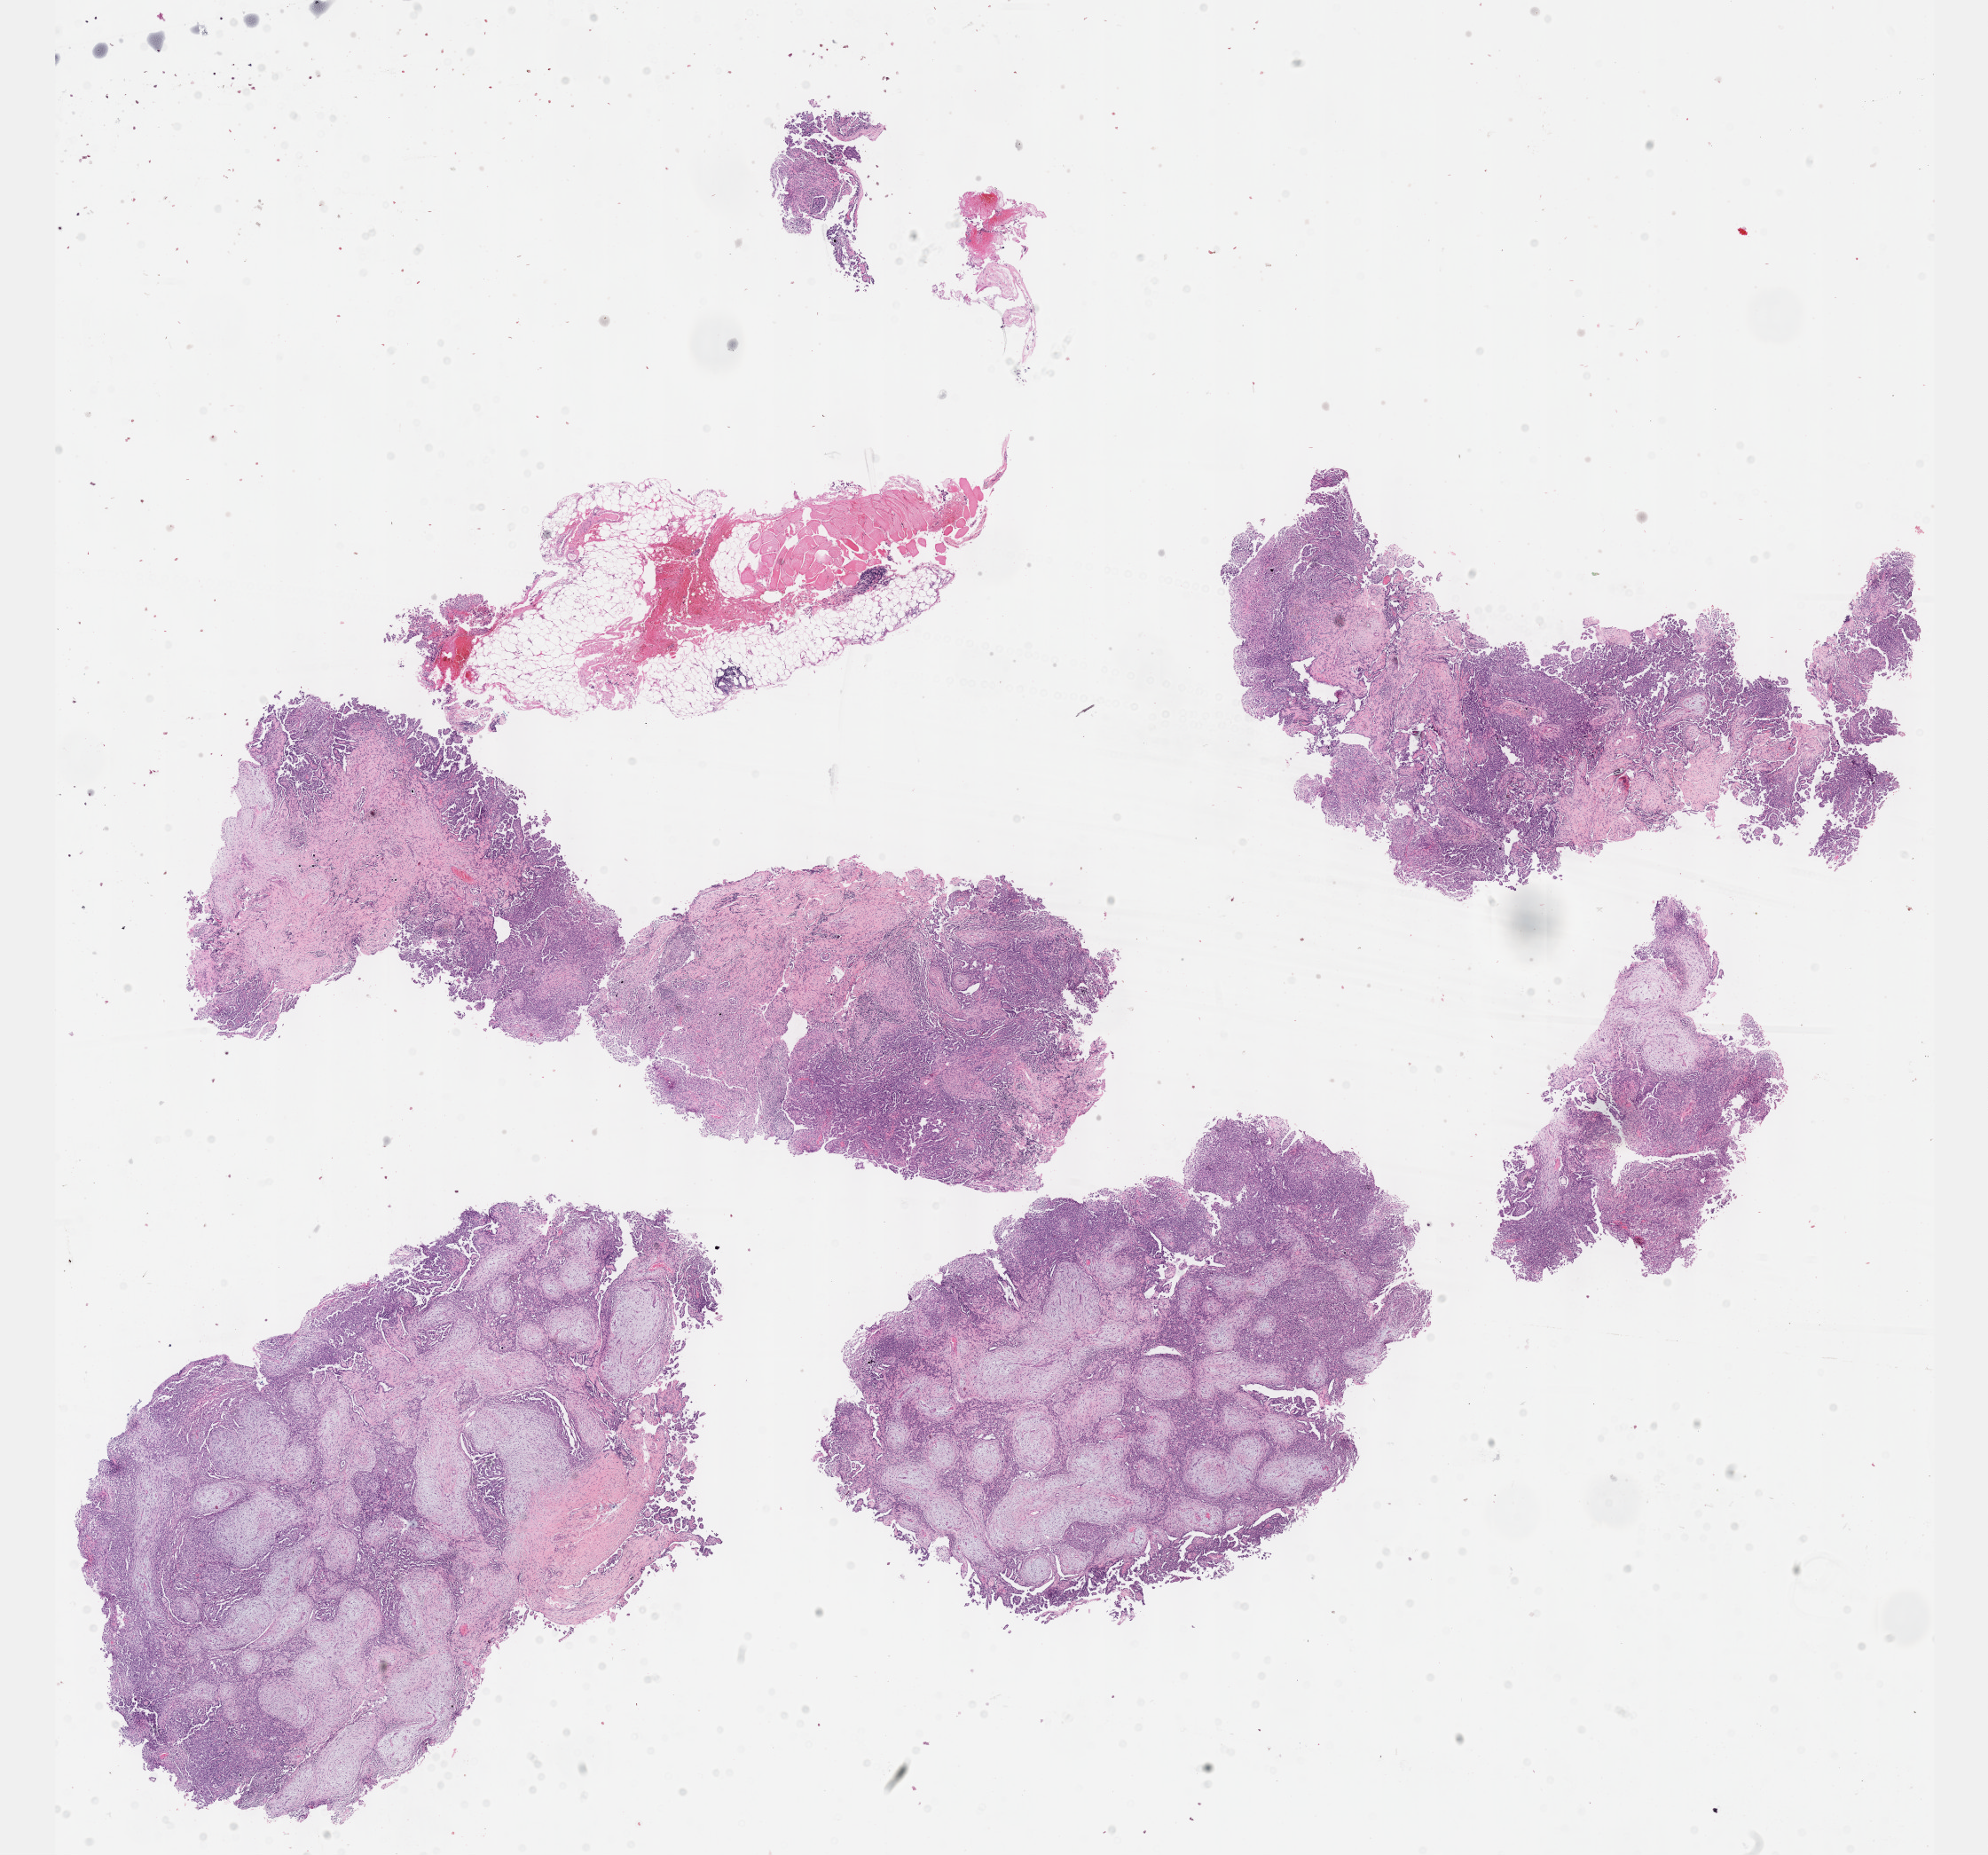
H&E-stained whole-slide image — shown as a low-resolution overview of the whole scanned area (about 18.1 x 16.9 mm, slide scanned at 40x). Formalin-fixed paraffin-embedded (FFPE) diagnostic section. Mesothelium, primary tumour sample. Patient: male, age at initial diagnosis 73 years.
* laterality: right
* diagnosis: Mesothelioma, biphasic, malignant (pleura, NOS)
* AJCC pathologic stage: III (7th edition)